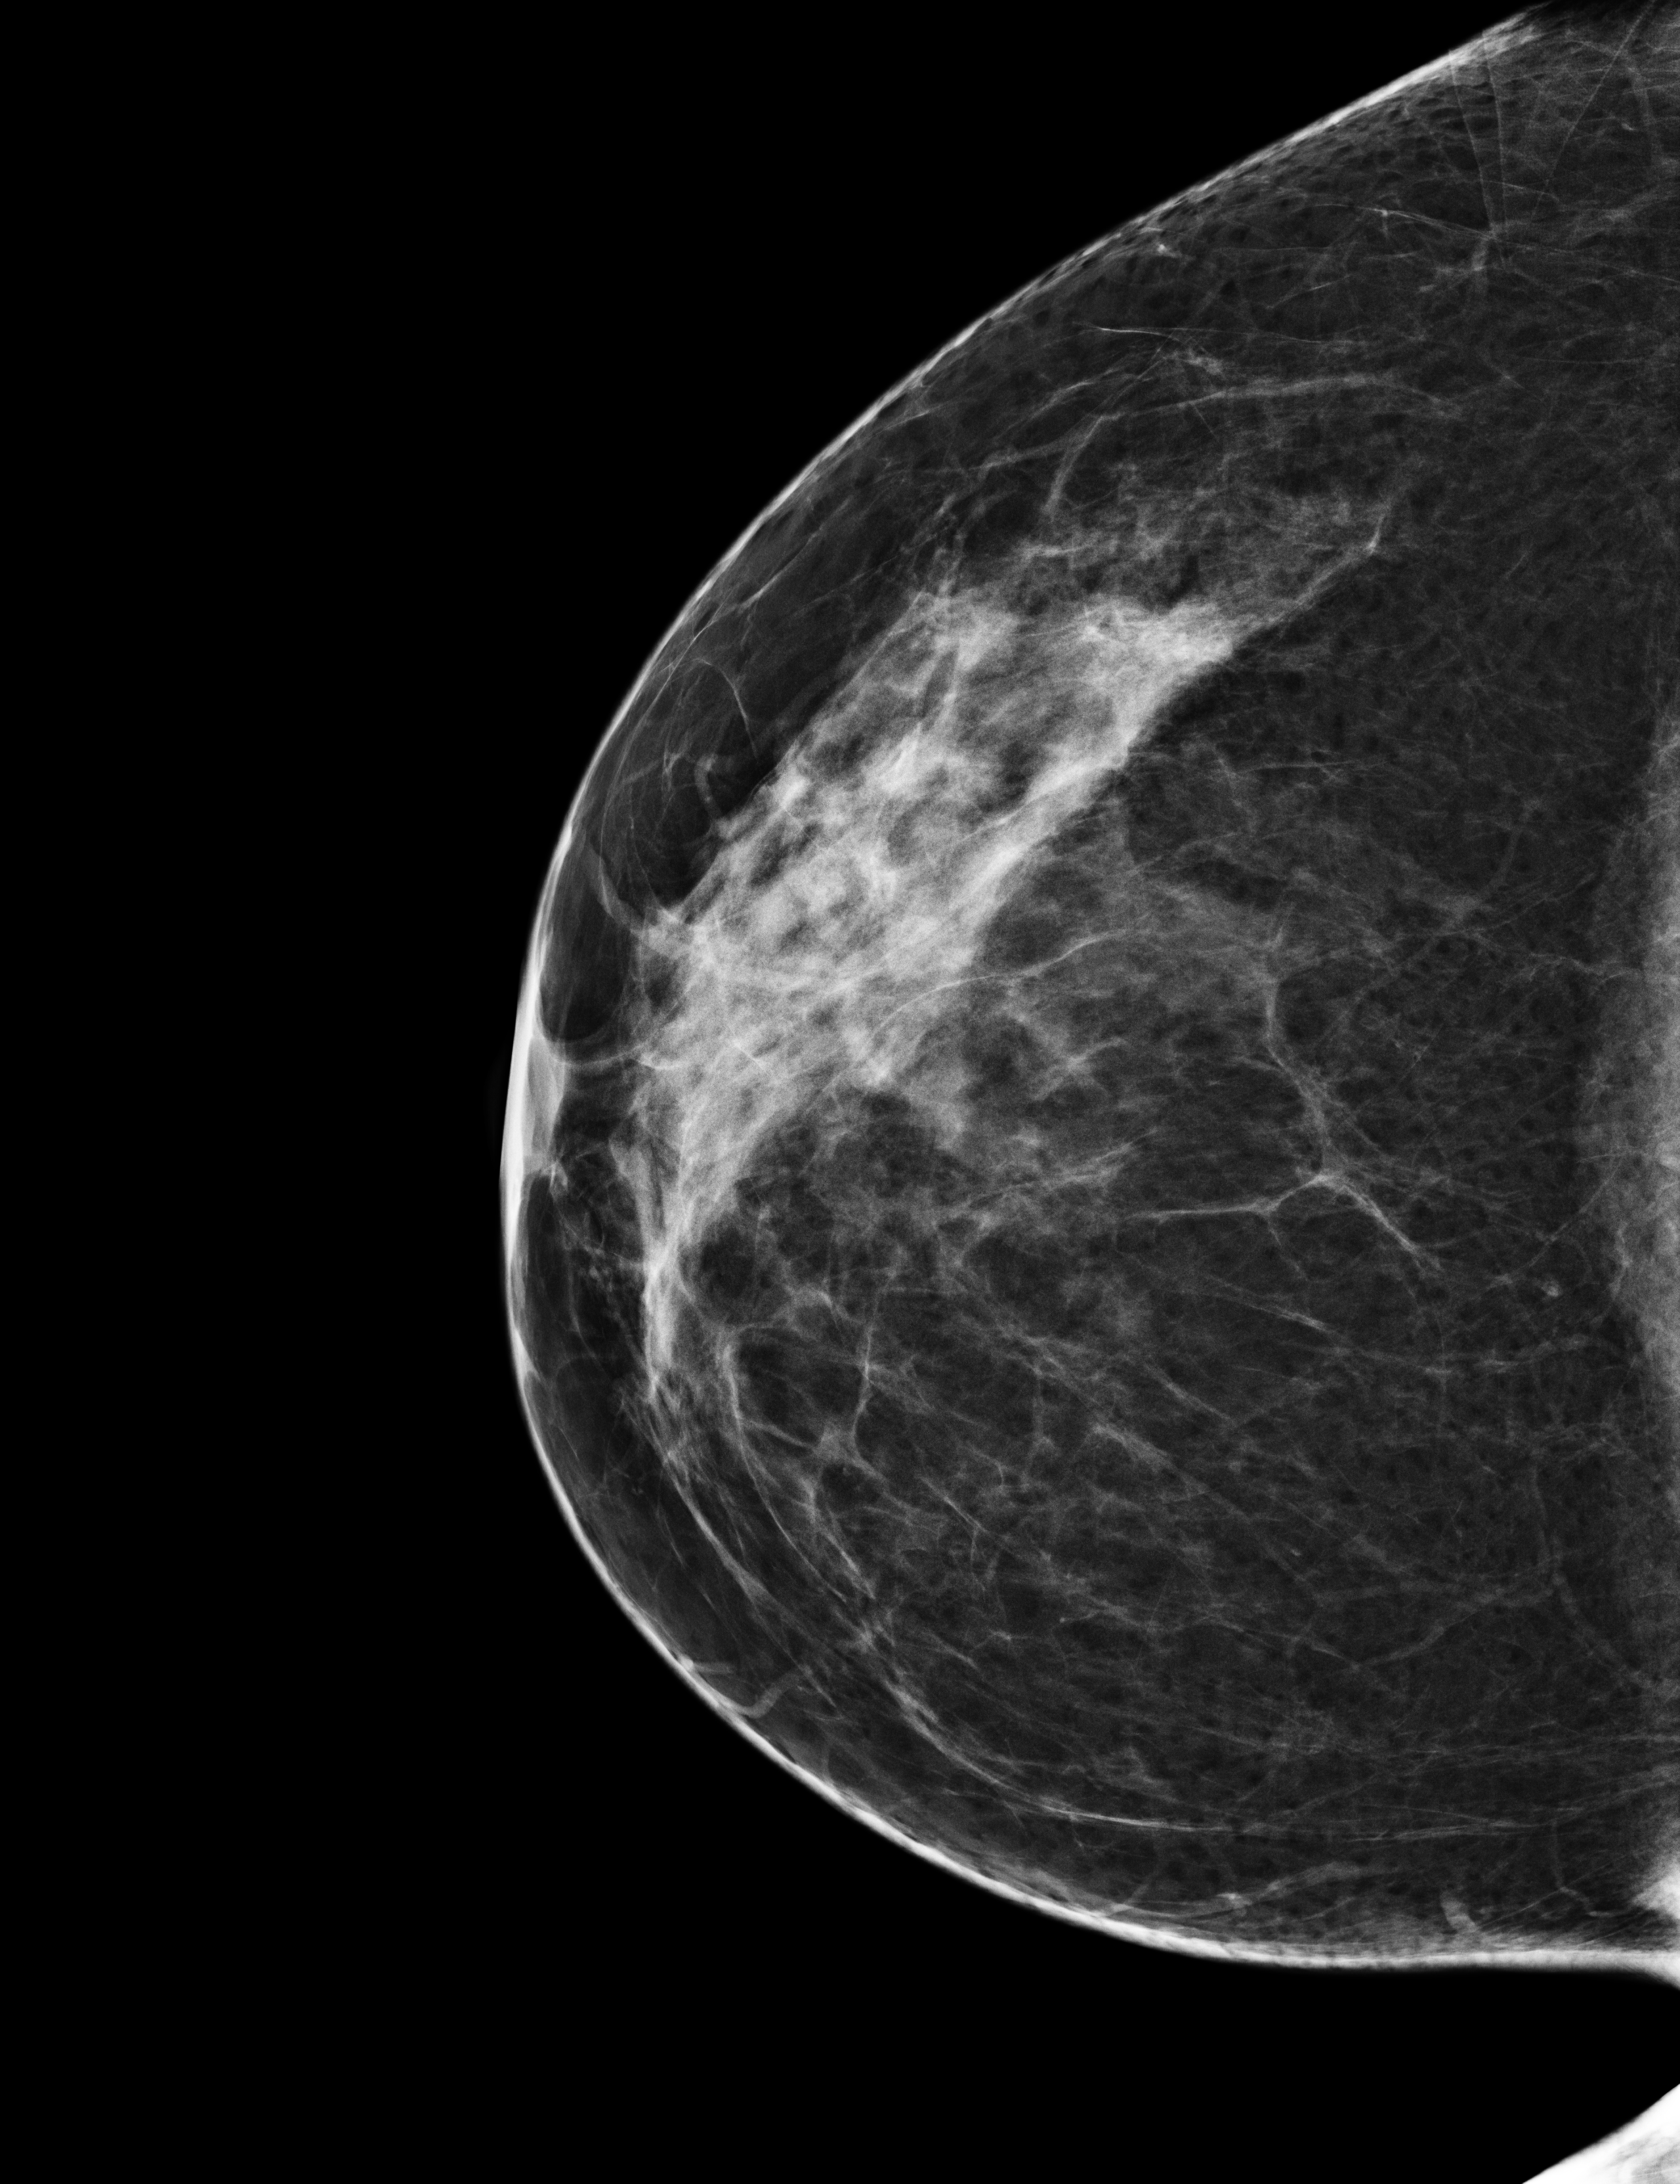
Annual screening mammography examination; compressed breast thickness 56 mm; system: Selenia Dimensions. Patient aged 42 years (female).
Image type: full-field digital mammogram. Breast: right. Projection: CC view.